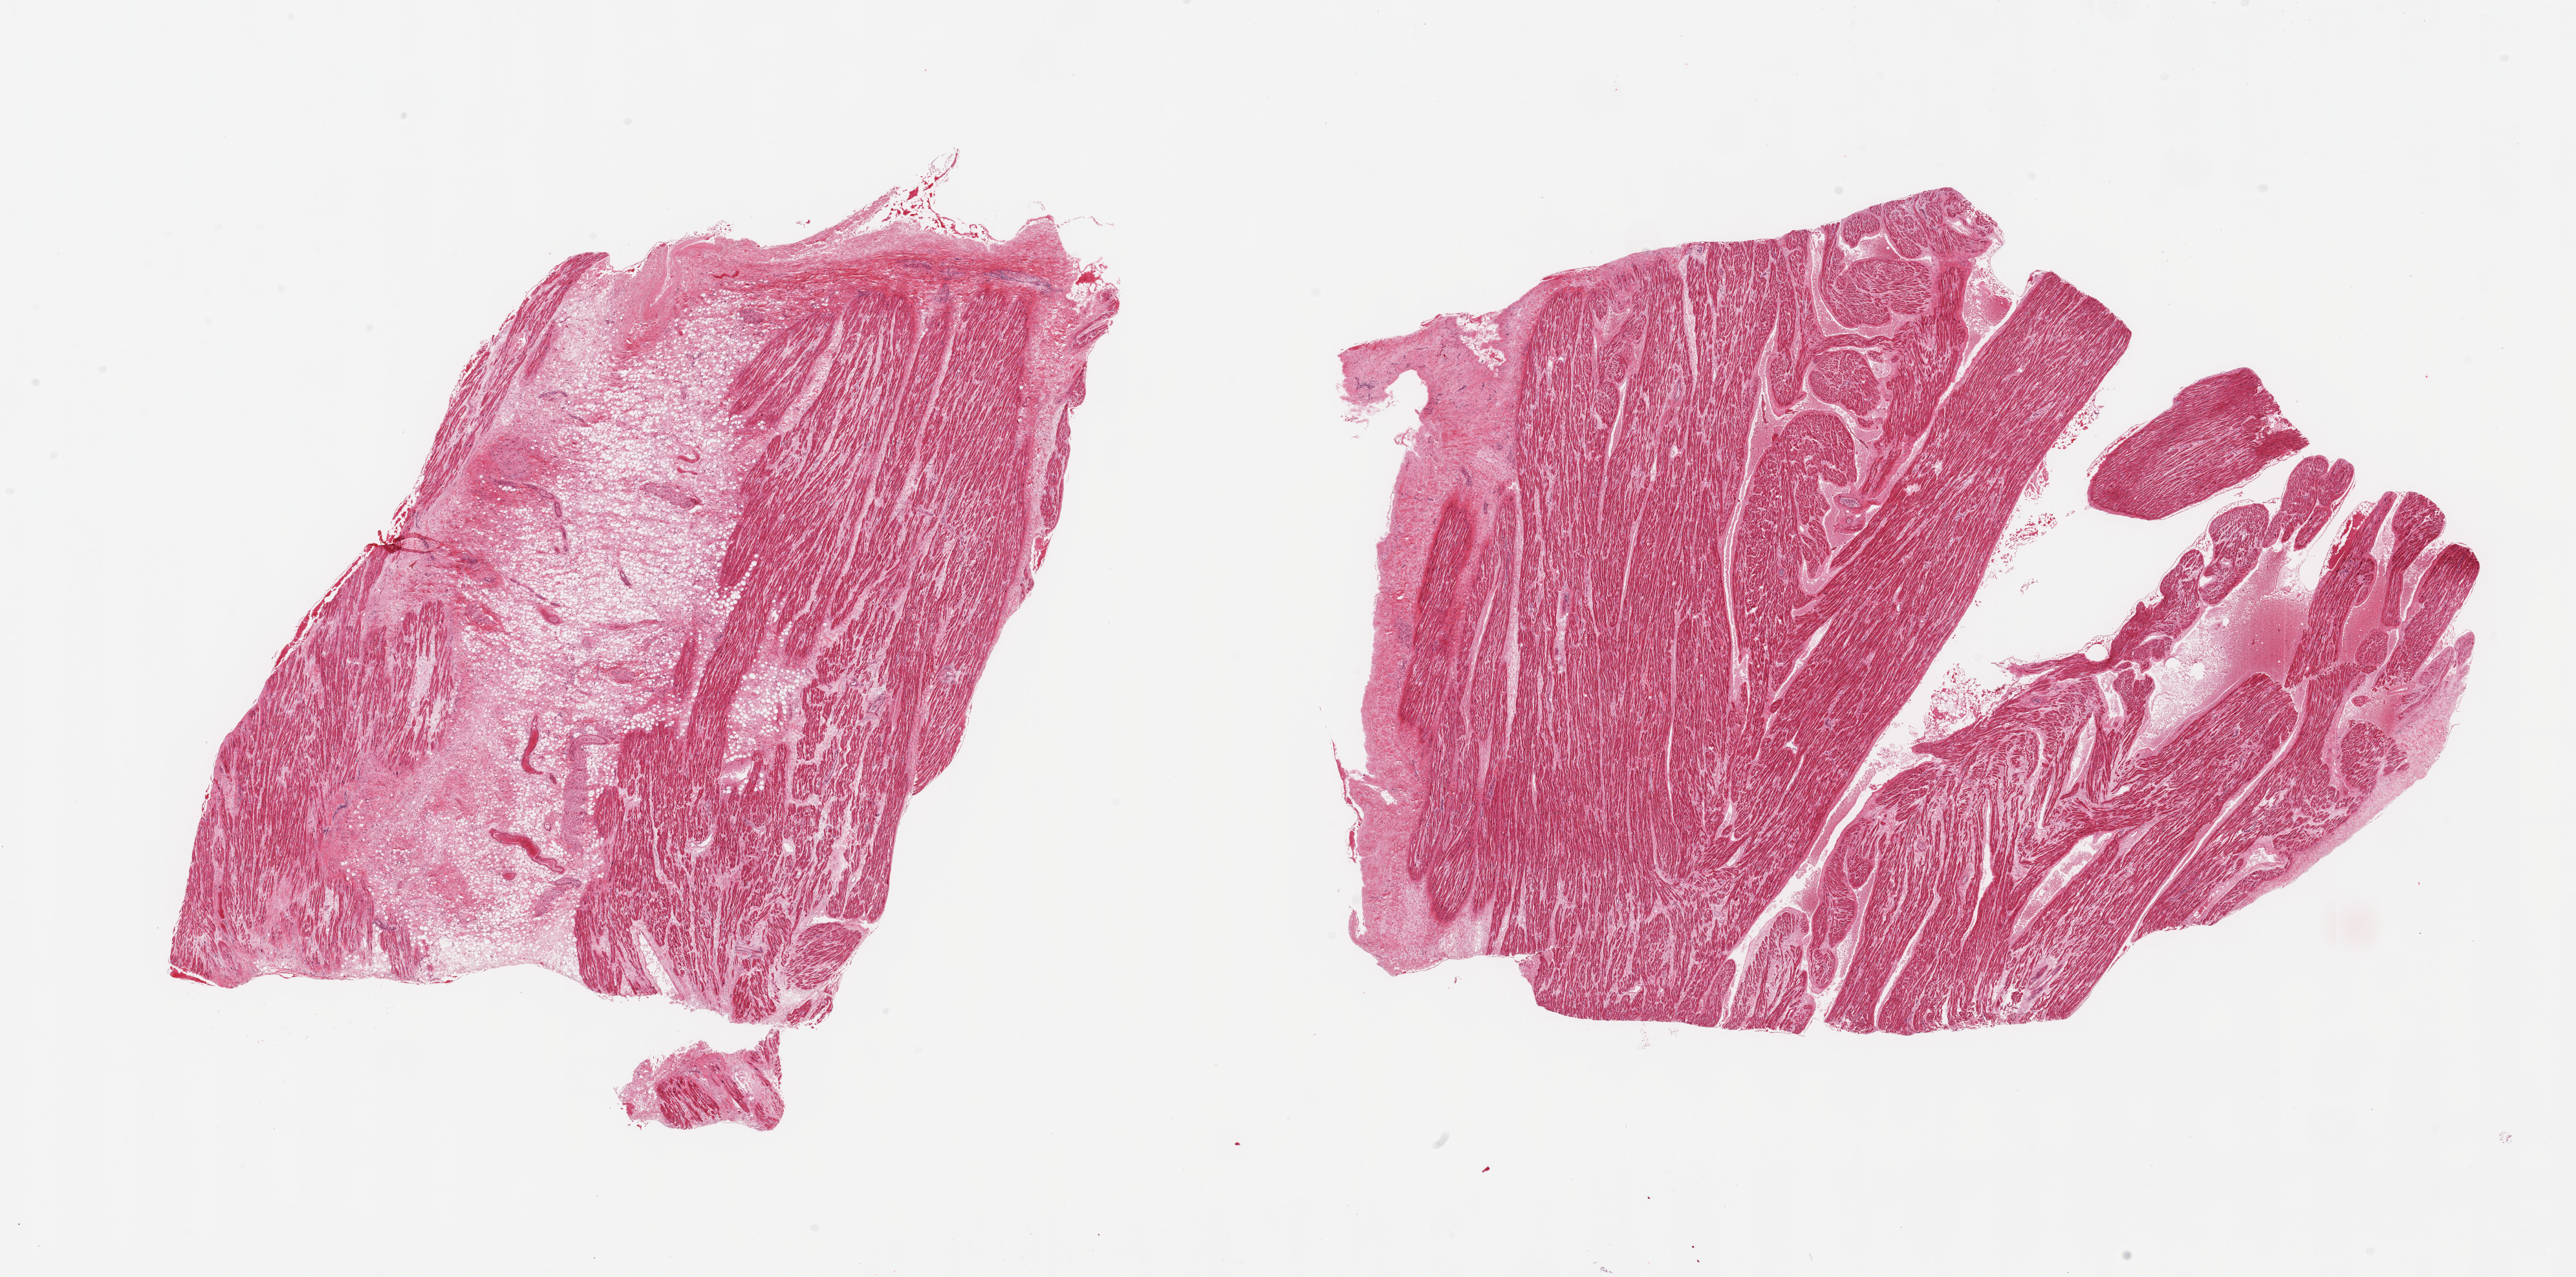
Hematoxylin and eosin (H&E) whole-slide image, a low-resolution overview of the entire scanned area, about 31.5 x 15.6 mm, PAXgene-fixed paraffin-embedded (PFPE) section, target tissue: auricular appendage, donor tissue sample. Donor sex: female.
Review note (as recorded): 2 pieces: 1 with 50% fibrofatty internal component.